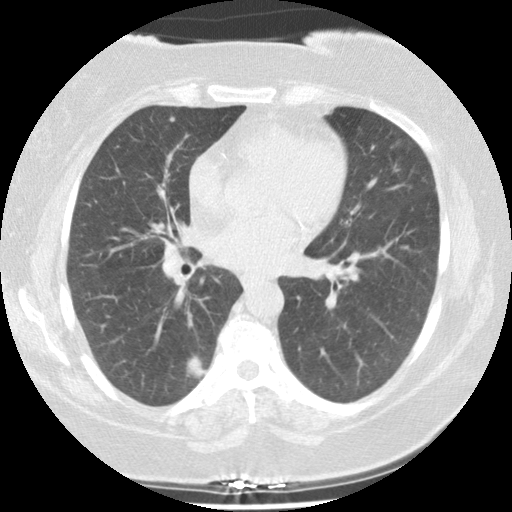
Low-dose screening chest CT, one axial slice; slice 76 of 131 in the series (ordered by position); reconstruction kernel STANDARD; 140 kVp; lung window (W 1500 / L -600 HU); 512 × 512 image matrix, field of view 320 × 320 mm.
Annotated regions visible in this slice (manually delineated by an expert):
- lesion 1 (tumor, lower lobe of right lung): bounding box [x1, y1, x2, y2] px = [187, 356, 208, 379]